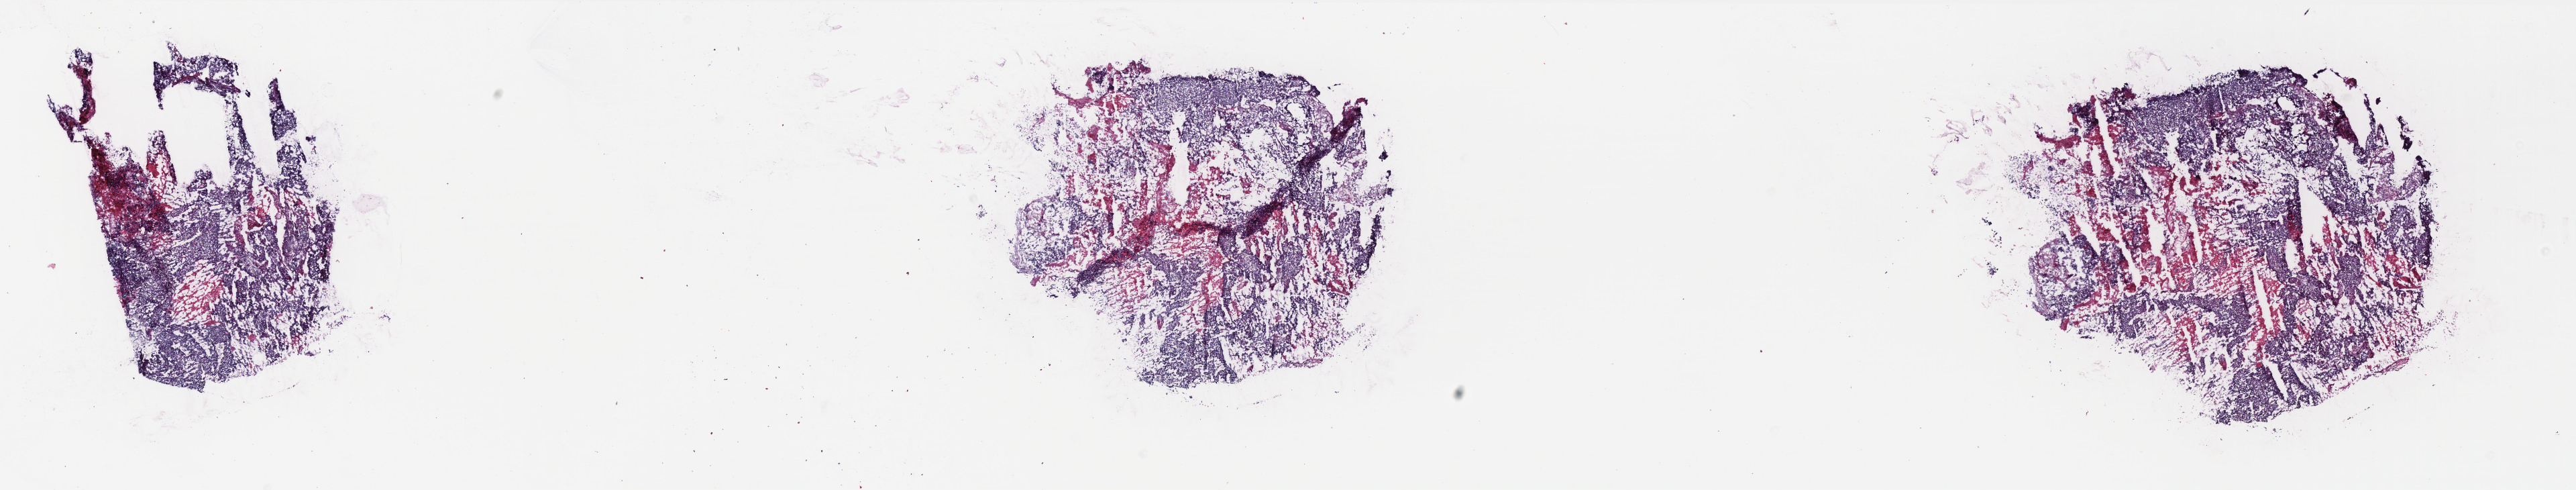
Digitized H&E-stained tissue section (whole slide) — a low-resolution overview of the entire scanned area, about 30.8 x 5.9 mm (from a 40x scan). Frozen section. Primary tumour sample from the uterus. Female patient; age at initial diagnosis 57 years. Histologic grade: G2 (moderately differentiated). Composition of this section per pathologist review: tumour cells 70%, tumour nuclei 90%, normal cells 0%, stromal cells 0%, necrosis 30%. Inflammatory infiltration, as recorded: lymphocyte infiltration 0%, monocyte infiltration 0%, neutrophil infiltration 0%.
FIGO stage: IB. Histologic diagnosis: Endometrioid adenocarcinoma, NOS (endometrium).